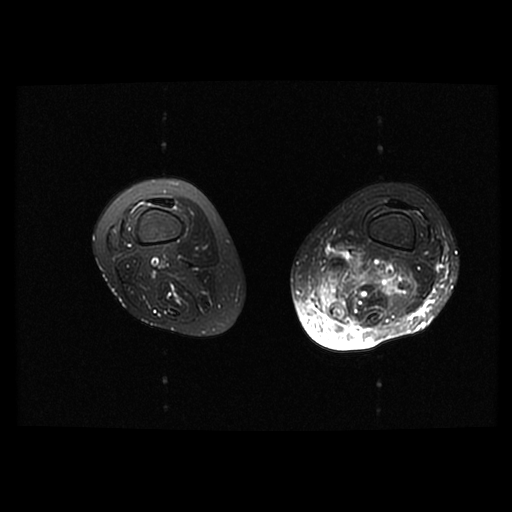
MRI of an extremity soft-tissue mass, one axial slice. Position 17 of 42 along the scan axis. T2-weighted fat-saturated. 6 mm slice thickness. 512 × 512 image matrix, field of view 420 × 420 mm. Female patient. From the clinical record (not read from this slice): histological type: pleomorphic leiomyosarcoma; grade: high; site of the primary tumour: left thigh.
Structures marked on this image (outlined manually by an expert reader):
- gross tumour volume including surrounding oedema: bounding box [x1, y1, x2, y2] px = [313, 250, 412, 322]